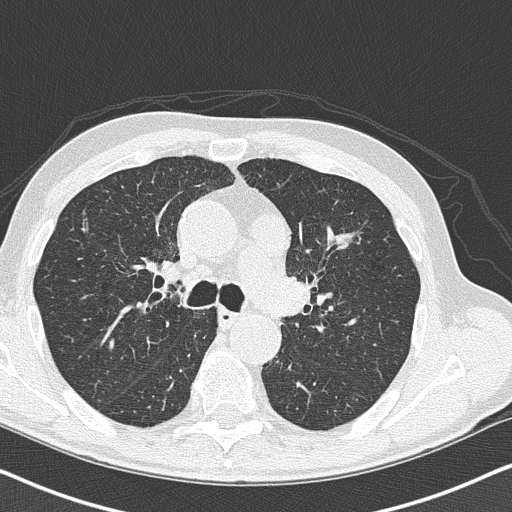
Axial slice from a low-dose chest CT screening exam. Second screening round (one year after baseline). Lung window (W 1500 / L -600 HU). Lung (sharp) reconstruction kernel (B50f). 512 × 512 image matrix, field of view 330 × 330 mm. Male participant, aged 73 years at enrolment. Current smoker at enrolment.
Expert-annotated lung lesion, bounding box [x1, y1, x2, y2] px = [311, 216, 375, 270]. The screening reader recorded 3 non-calcified nodules or masses ≥4 mm on this exam (left upper lobe, left upper lobe, right lower lobe); which of them this box marks is not recorded. Official screen result: positive, other. Participant outcome: lung cancer diagnosed 36 days after this screen — small cell carcinoma, NOS, left upper lobe, stage IIIB (AJCC 6th edition), 19 mm at pathology.